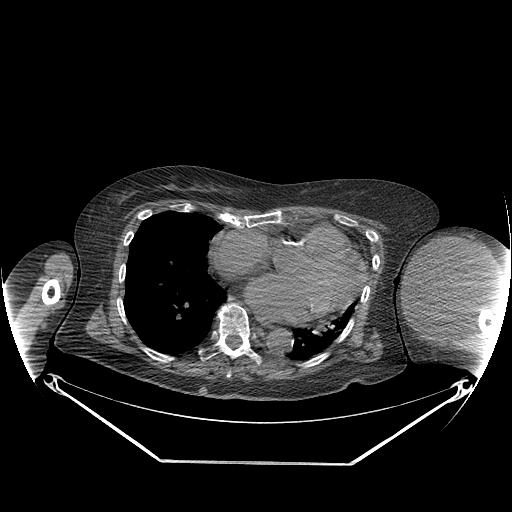
CT of an extremity soft-tissue mass (from a PET/CT study), one axial slice; slice 160 of 267 in the series (ordered by position); reconstruction kernel STANDARD; 140 kVp; soft-tissue window (W 400 / L 40 HU); 3.75 mm slice thickness; 512 × 512 image matrix, field of view 500 × 500 mm. Female patient. Case-level facts recorded for this patient, not image findings: histological type: pleiomorphic leiomyosarcoma; grade: high; site of the primary tumour: left biceps.
Outlined on this slice (expert contour drawn on MRI and transferred to this co-registered scan by the dataset authors):
- gross tumour volume including surrounding oedema: box from (x=402, y=235) to (x=494, y=330) px
- gross tumour volume (mass): (x=402, y=237)–(x=492, y=330)